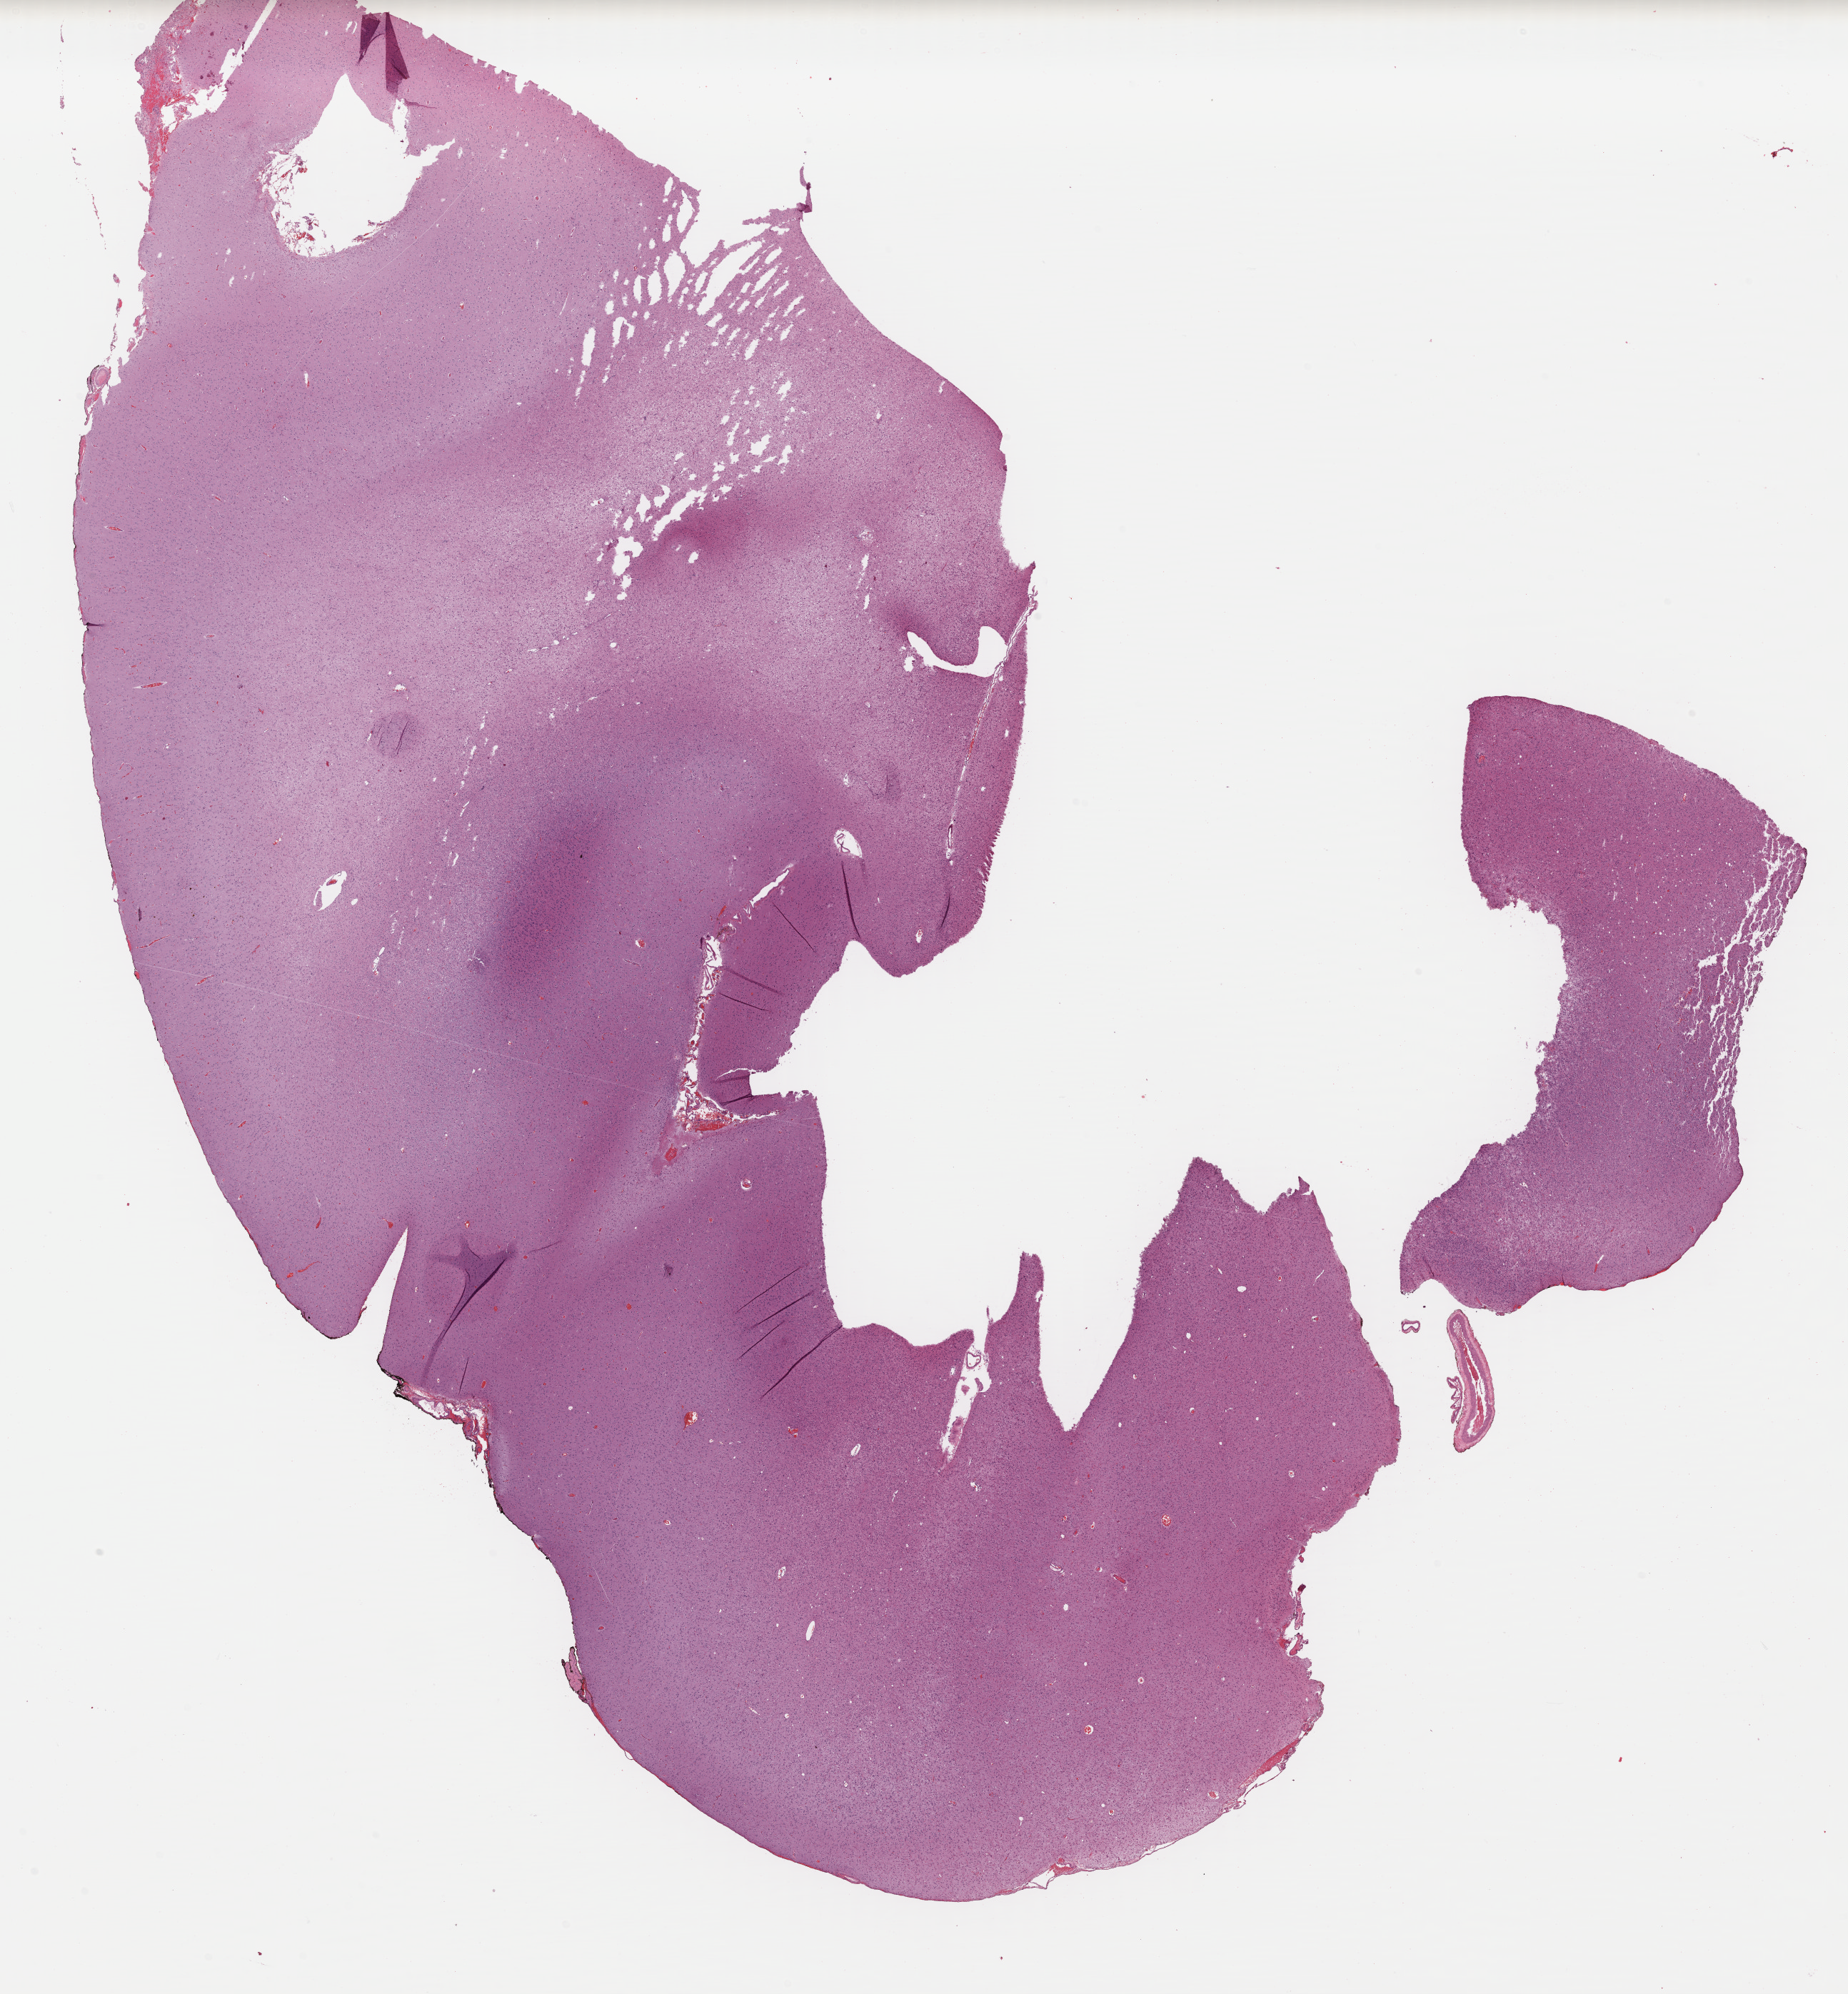
Whole-slide histology image, H&E — low-resolution overview of the scanned area, about 20.3 x 22.0 mm. Formalin-fixed paraffin-embedded (FFPE) diagnostic section. Brain, primary tumour sample. Female patient; age at initial diagnosis 61 years. Histologic grade: G2 (moderately differentiated).
Histologic diagnosis: Astrocytoma, NOS (cerebrum).